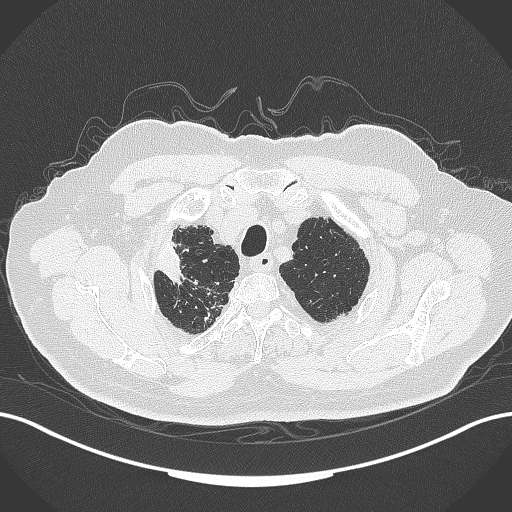
Chest CT, one axial slice. Slice 314 of 389 in the series (ordered by position). Reconstruction kernel B70f. 120 kVp. Lung window (W 1500 / L -600 HU). 512 × 512 image matrix, field of view 400 × 400 mm. Patient: male, 72 years. Case-level facts recorded for this patient, not image findings: clinical TNM (as recorded): T1a N0 M0.
Annotated regions visible in this slice (rectangle marked by the reading radiologist):
- lung tumour (recorded histology: squamous cell carcinoma): box from (x=158, y=236) to (x=191, y=287) px